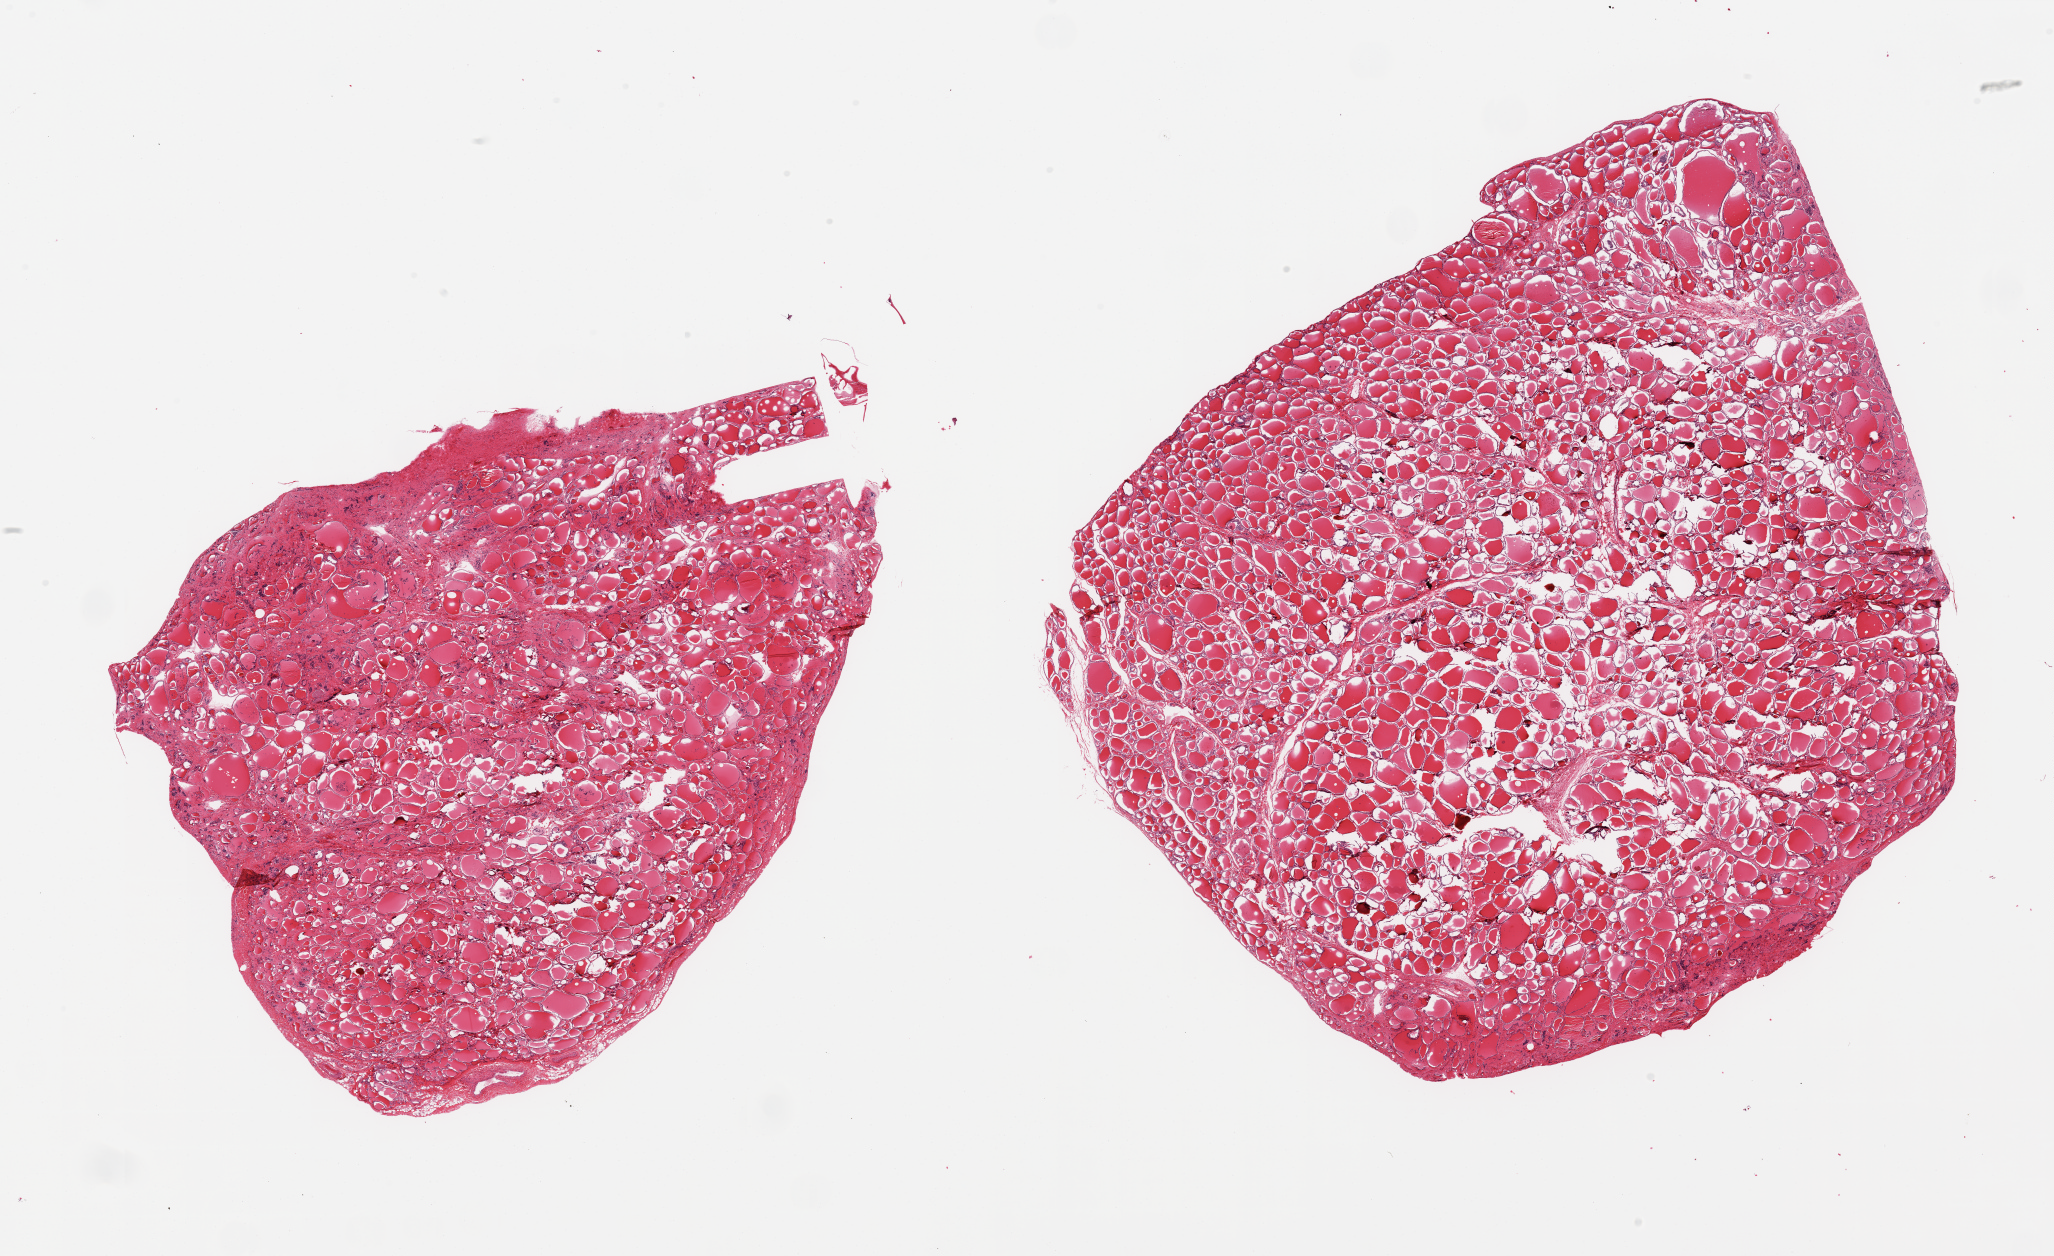
Digitized H&E-stained section, shown as a low-resolution overview of the whole scanned area (about 32.5 x 19.9 mm, slide scanned at 20x); PAXgene-fixed, paraffin-embedded tissue; sampled site (target tissue): thyroid; donor tissue sample. Donor sex: male.
Reviewer comment on this tissue sample: 2 pieces, no abnormalities.